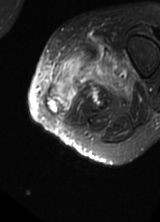
MRI of an extremity soft-tissue mass, one axial slice. Position 13 of 69 along the scan axis. T2-weighted fat-saturated. MR volume resampled by the dataset authors to the PET/CT grid (not the native acquisition matrix). 160 × 222 image matrix. Female patient. From the clinical record (not read from this slice): histological type: pleomorphic leiomyosarcoma; grade: high; site of the primary tumour: left thigh.
Annotated regions visible in this slice (expert contour drawn on MRI and transferred to this co-registered scan by the dataset authors):
- gross tumour volume including surrounding oedema: bounding box <47,47,133,115> (left, top, right, bottom; pixels)
- gross tumour volume (mass): <48,100,69,115>